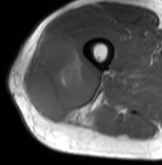
MRI of an extremity soft-tissue mass, one axial slice. Slice 41 of 61 in the series (ordered by position). MR volume resampled by the dataset authors to the PET/CT grid (not the native acquisition matrix). 162 × 165 image matrix, field of view 158 × 161 mm. Male patient. Case-level facts recorded for this patient, not image findings: histological type: poorly differentiated synovial sarcoma; grade: high; site of the primary tumour: right buttock.
Structures marked on this image (expert contour drawn on MRI and transferred to this co-registered scan by the dataset authors):
- gross tumour volume including surrounding oedema: bounding box [x1, y1, x2, y2] px = [23, 33, 101, 124]
- gross tumour volume (mass): [23, 33, 99, 121]